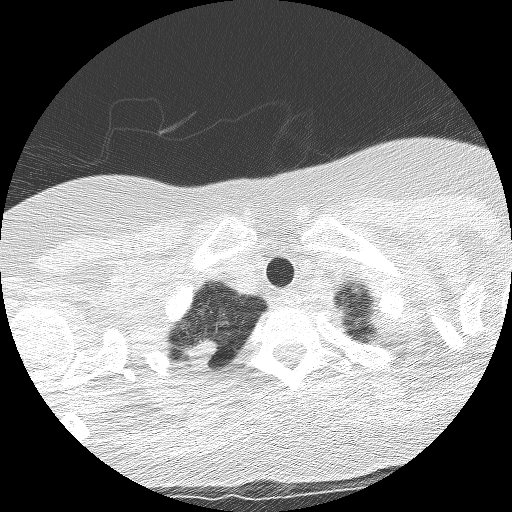
Axial slice from a low-dose chest CT screening exam. Third annual screen. Lung window (W 1500 / L -600 HU). Lung (sharp) reconstruction kernel (BONE). 512 × 512 image matrix, field of view 290 × 290 mm. Female, age 56 years at enrolment. Current smoker at enrolment.
Expert-annotated lung lesion, bounding box [x1, y1, x2, y2] px = [171, 327, 226, 374]. Reader record for this screening exam (exam-level; its link to the box is not recorded): non-calcified nodule or mass ≥4 mm, right upper lobe, 17 × 10 mm, spiculated (stellate) margins, mixed attenuation, pre-existing on the prior screen: yes; interval growth: yes. Participant outcome: lung cancer diagnosed 24 days after this screen — large cell carcinoma, NOS, right upper lobe, poorly differentiated (G3), stage IB (AJCC 6th edition), 15 mm at pathology.